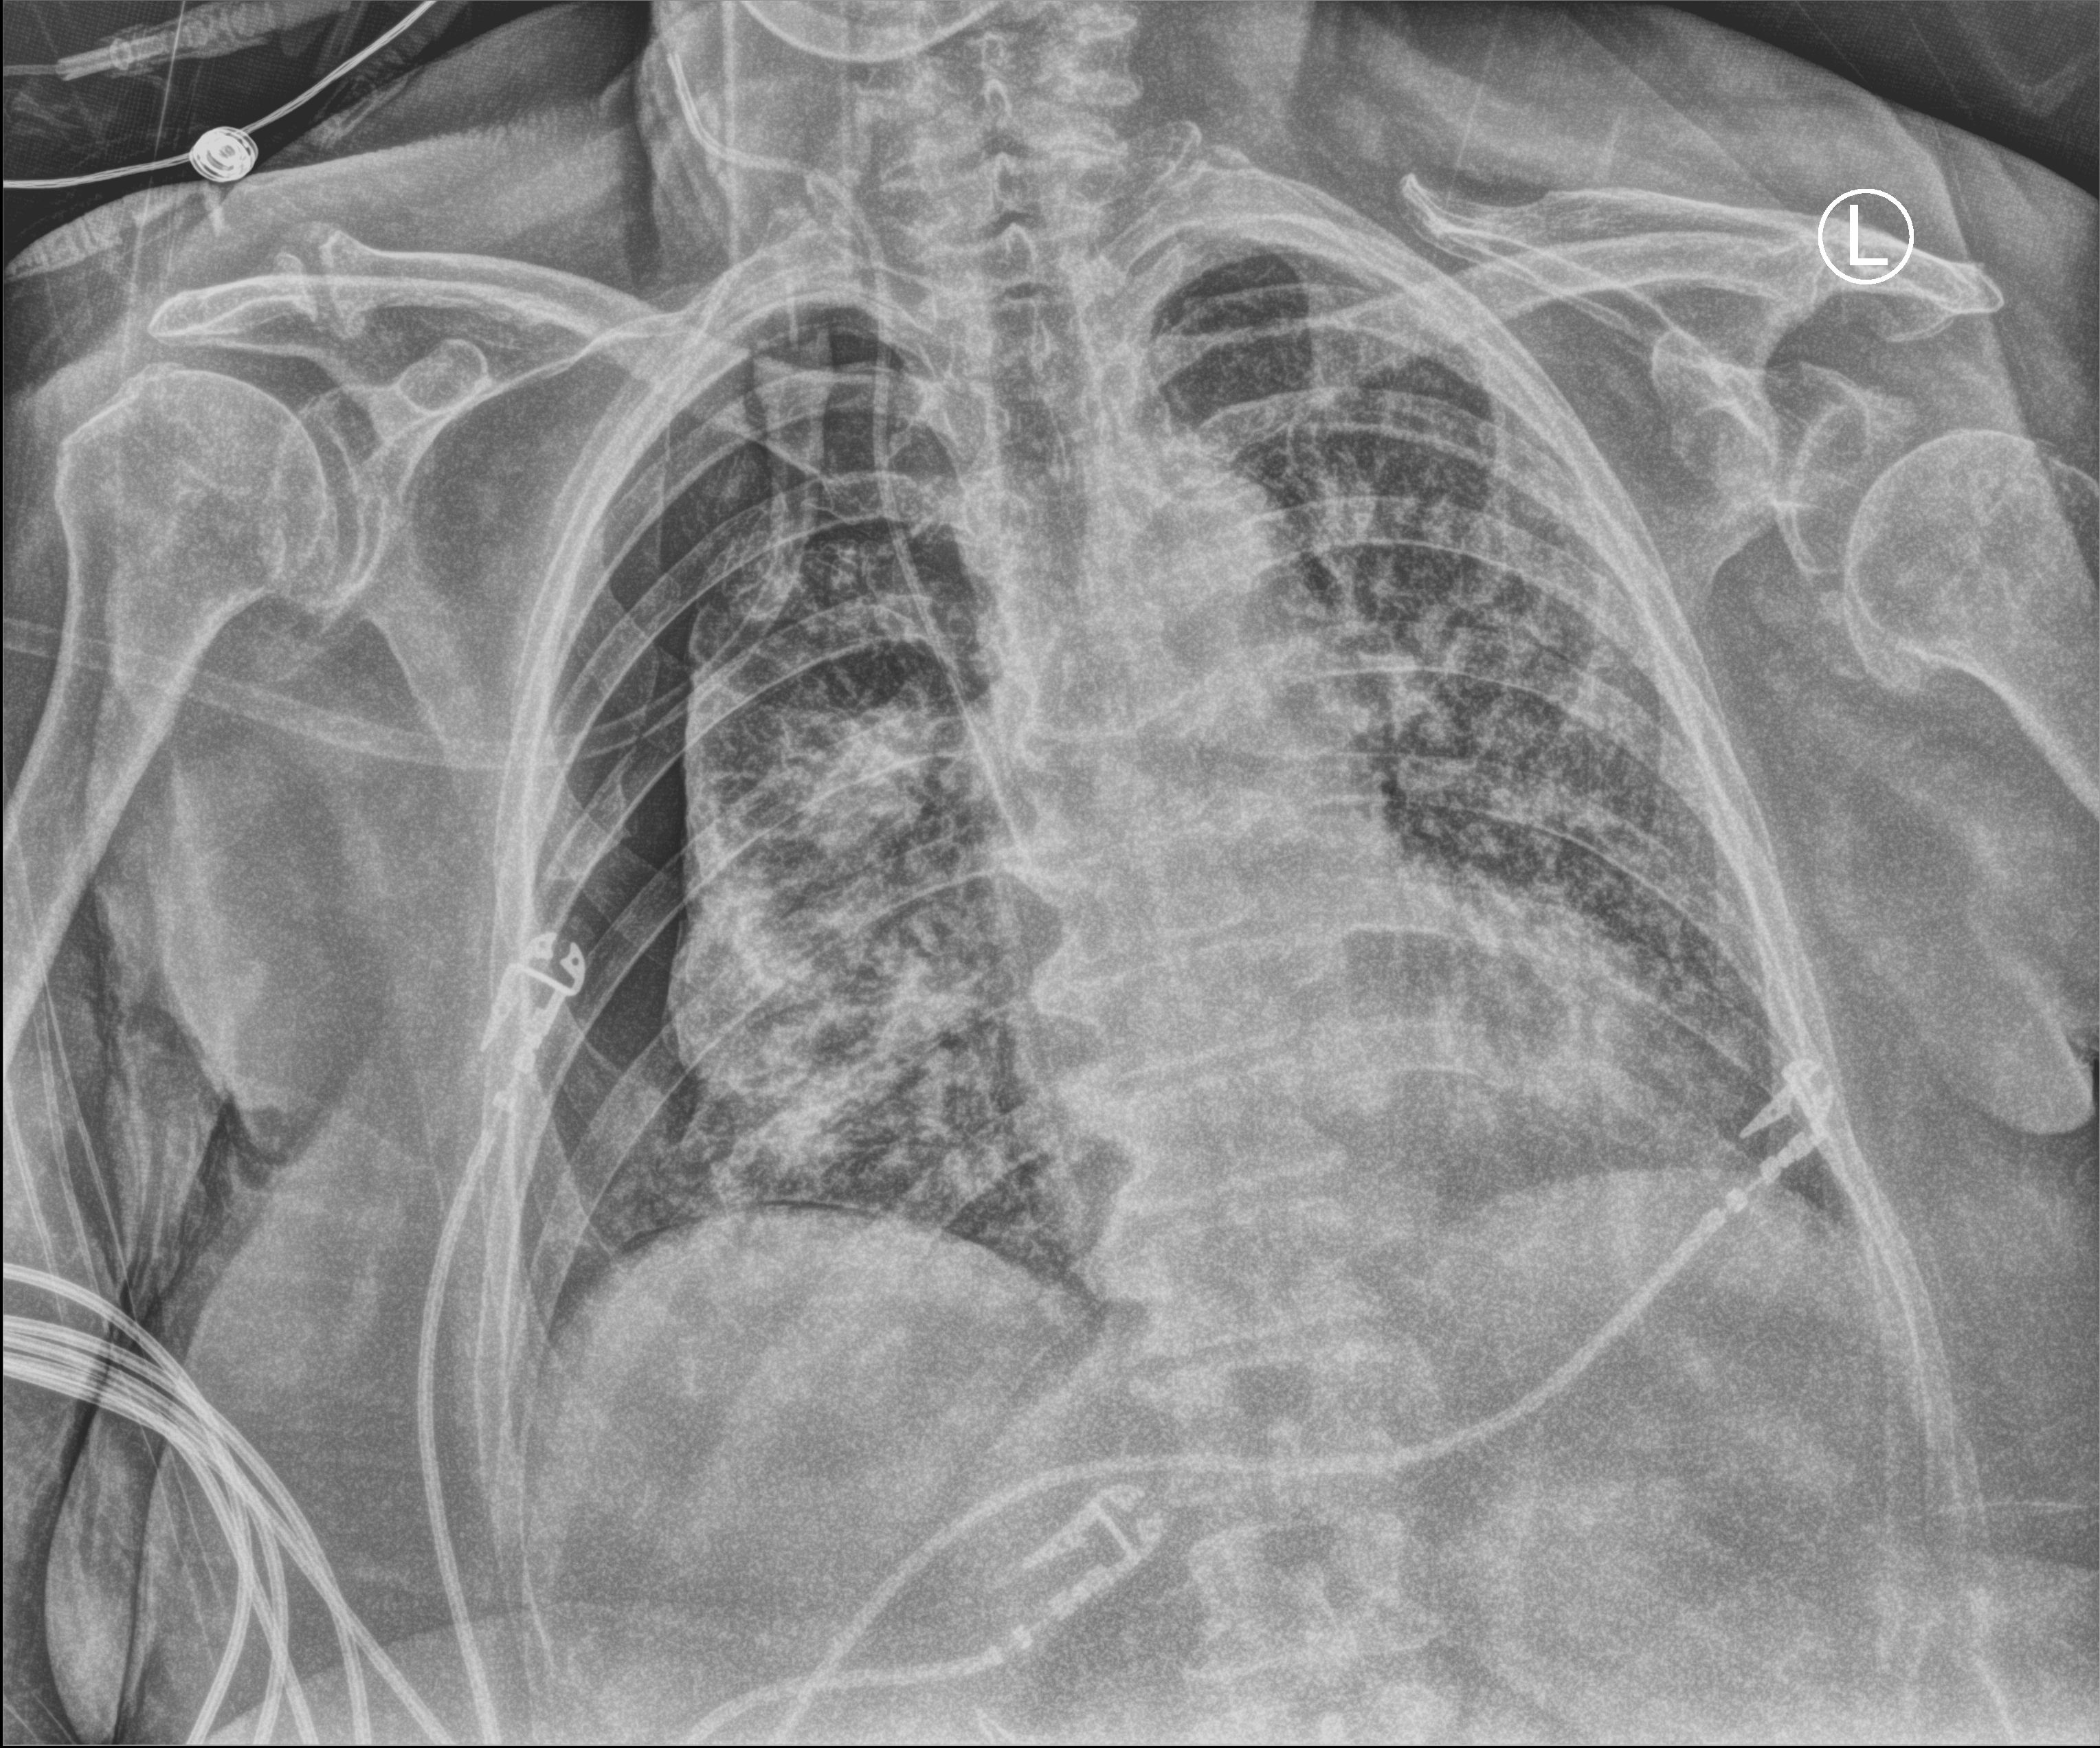
Portable chest radiograph; anteroposterior (AP) projection. Patient hospitalised with COVID-19; female, aged 75–90 years.
From the hospital-stay record, not from the radiograph (when in the stay this image was taken is not recorded): mechanically ventilated during this hospital stay: yes; admitted to intensive care during this hospital stay: no.